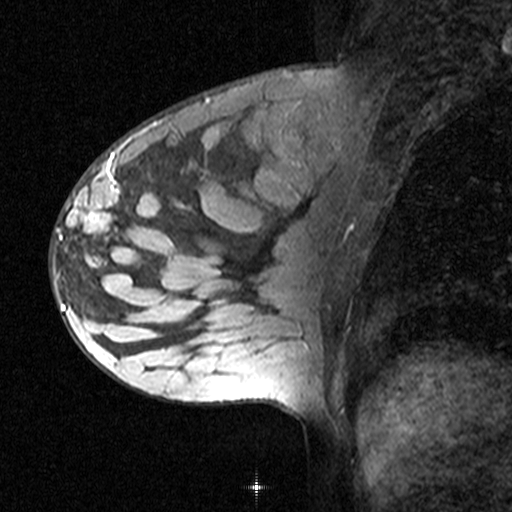
Breast MRI (dynamic contrast-enhanced), one sagittal slice; dynamic contrast-enhanced study with each time point stored as its own series, time point 2 of 3 at this slice position (early post-contrast, ordered by acquisition time); 1.5 T; TE 4.5 ms, TR 11 ms; 3 mm slice thickness; 512 × 512 image matrix, field of view 200 × 200 mm. Patient: female, 27 years. Case-level facts recorded for this patient, not image findings: setting: breast cancer imaged before/during neoadjuvant chemotherapy; receptor status: HR-positive, HER2-negative.
Outlined on this slice (semi-automatic segmentation, software-assisted and operator-edited):
- analysis volume of interest (the breast-tissue region the enhancement analysis was run in; not a lesion): box from (x=51, y=162) to (x=163, y=271) px
- tumour enhancement mask (voxels above the 90 % enhancement threshold inside the analysis volume of interest): (x=56, y=188)–(x=142, y=258)